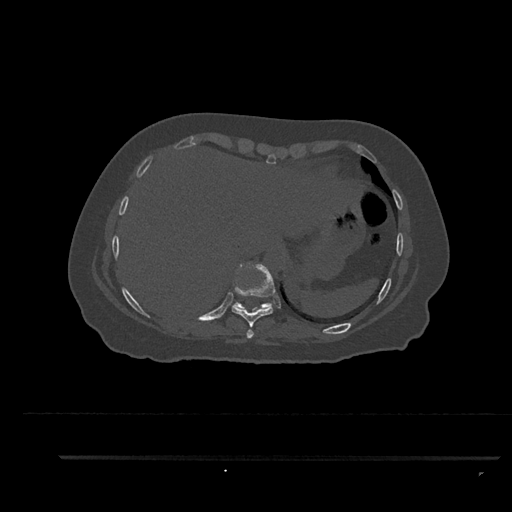
CT including the spine, one axial slice. Reconstruction kernel Br40s/3. 120 kVp. Bone window (W 1800 / L 400 HU). 0.5 mm slice thickness. 512 × 512 image matrix, field of view 408 × 408 mm. Female patient, age 44 years. Case-level facts recorded for this patient, not image findings: primary cancer: renal; vertebrae with lytic lesions (as recorded): L1.
Annotated regions visible in this slice (semi-automatic segmentation, software-assisted and operator-edited):
- T10 vertebra: box from (x=233, y=302) to (x=273, y=310) px
- T8 vertebra: (x=246, y=329)–(x=254, y=339)
- T9 vertebra: (x=232, y=263)–(x=274, y=328)